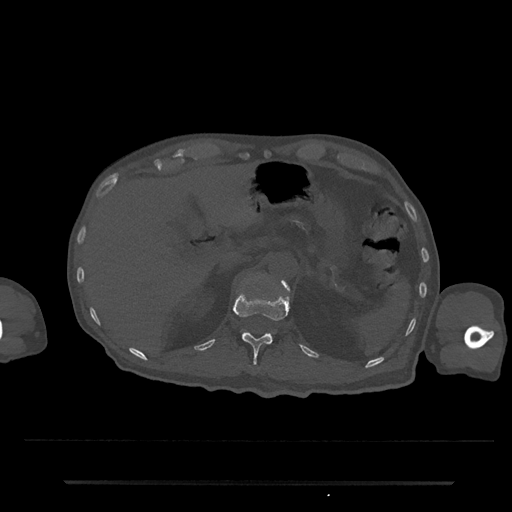
CT including the spine, one axial slice. Slice 182 of 797 in the series (ordered by position). Reconstruction kernel Br40s/3. Bone window (W 1800 / L 400 HU). 0.5 mm slice thickness. 512 × 512 image matrix. Male patient, age 74 years. From the clinical record (not read from this slice): primary cancer: prostate.
Annotated regions visible in this slice (semi-automatically segmented with operator editing):
- L1 vertebra: bounding box [x1, y1, x2, y2] px = [241, 280, 289, 335]
- T12 vertebra: [234, 293, 289, 364]